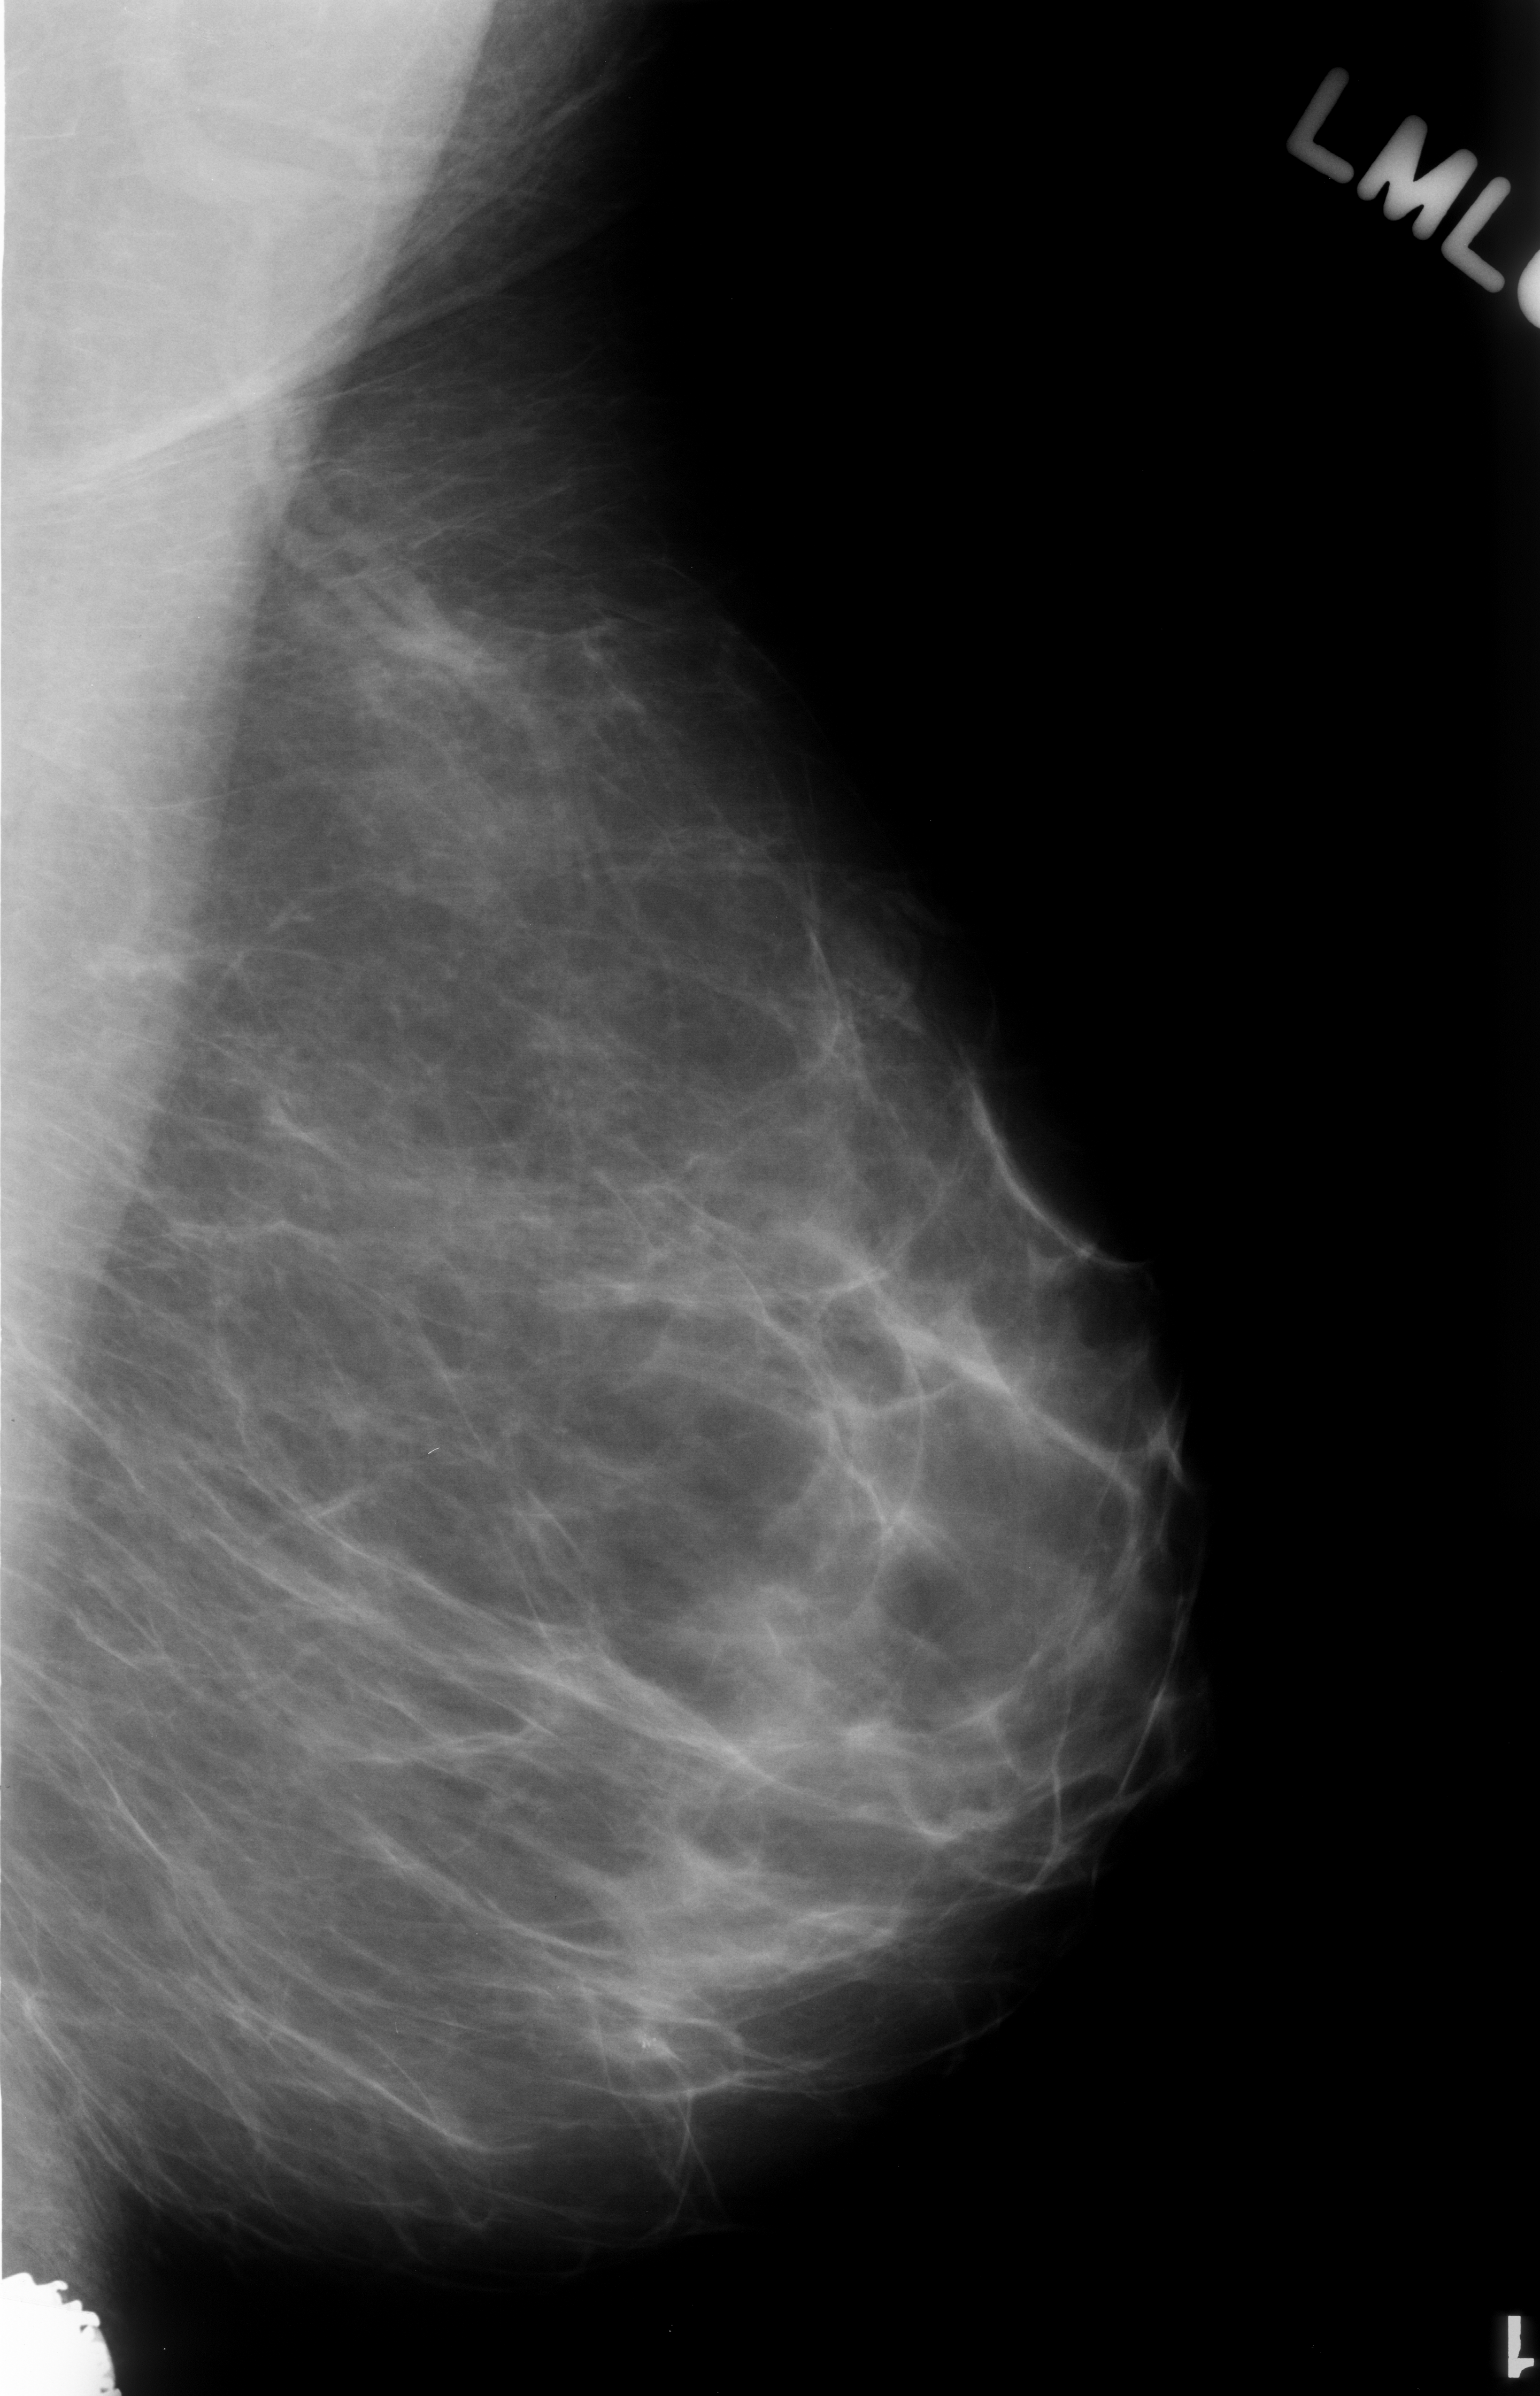
Digitized screen-film mammogram; left breast; MLO view; breast composition: almost entirely fatty (BI-RADS density category 1 of 4).
- Marked abnormality: calcifications, morphology pleomorphic, distribution clustered; BI-RADS assessment category 3; pathology (as recorded): benign.